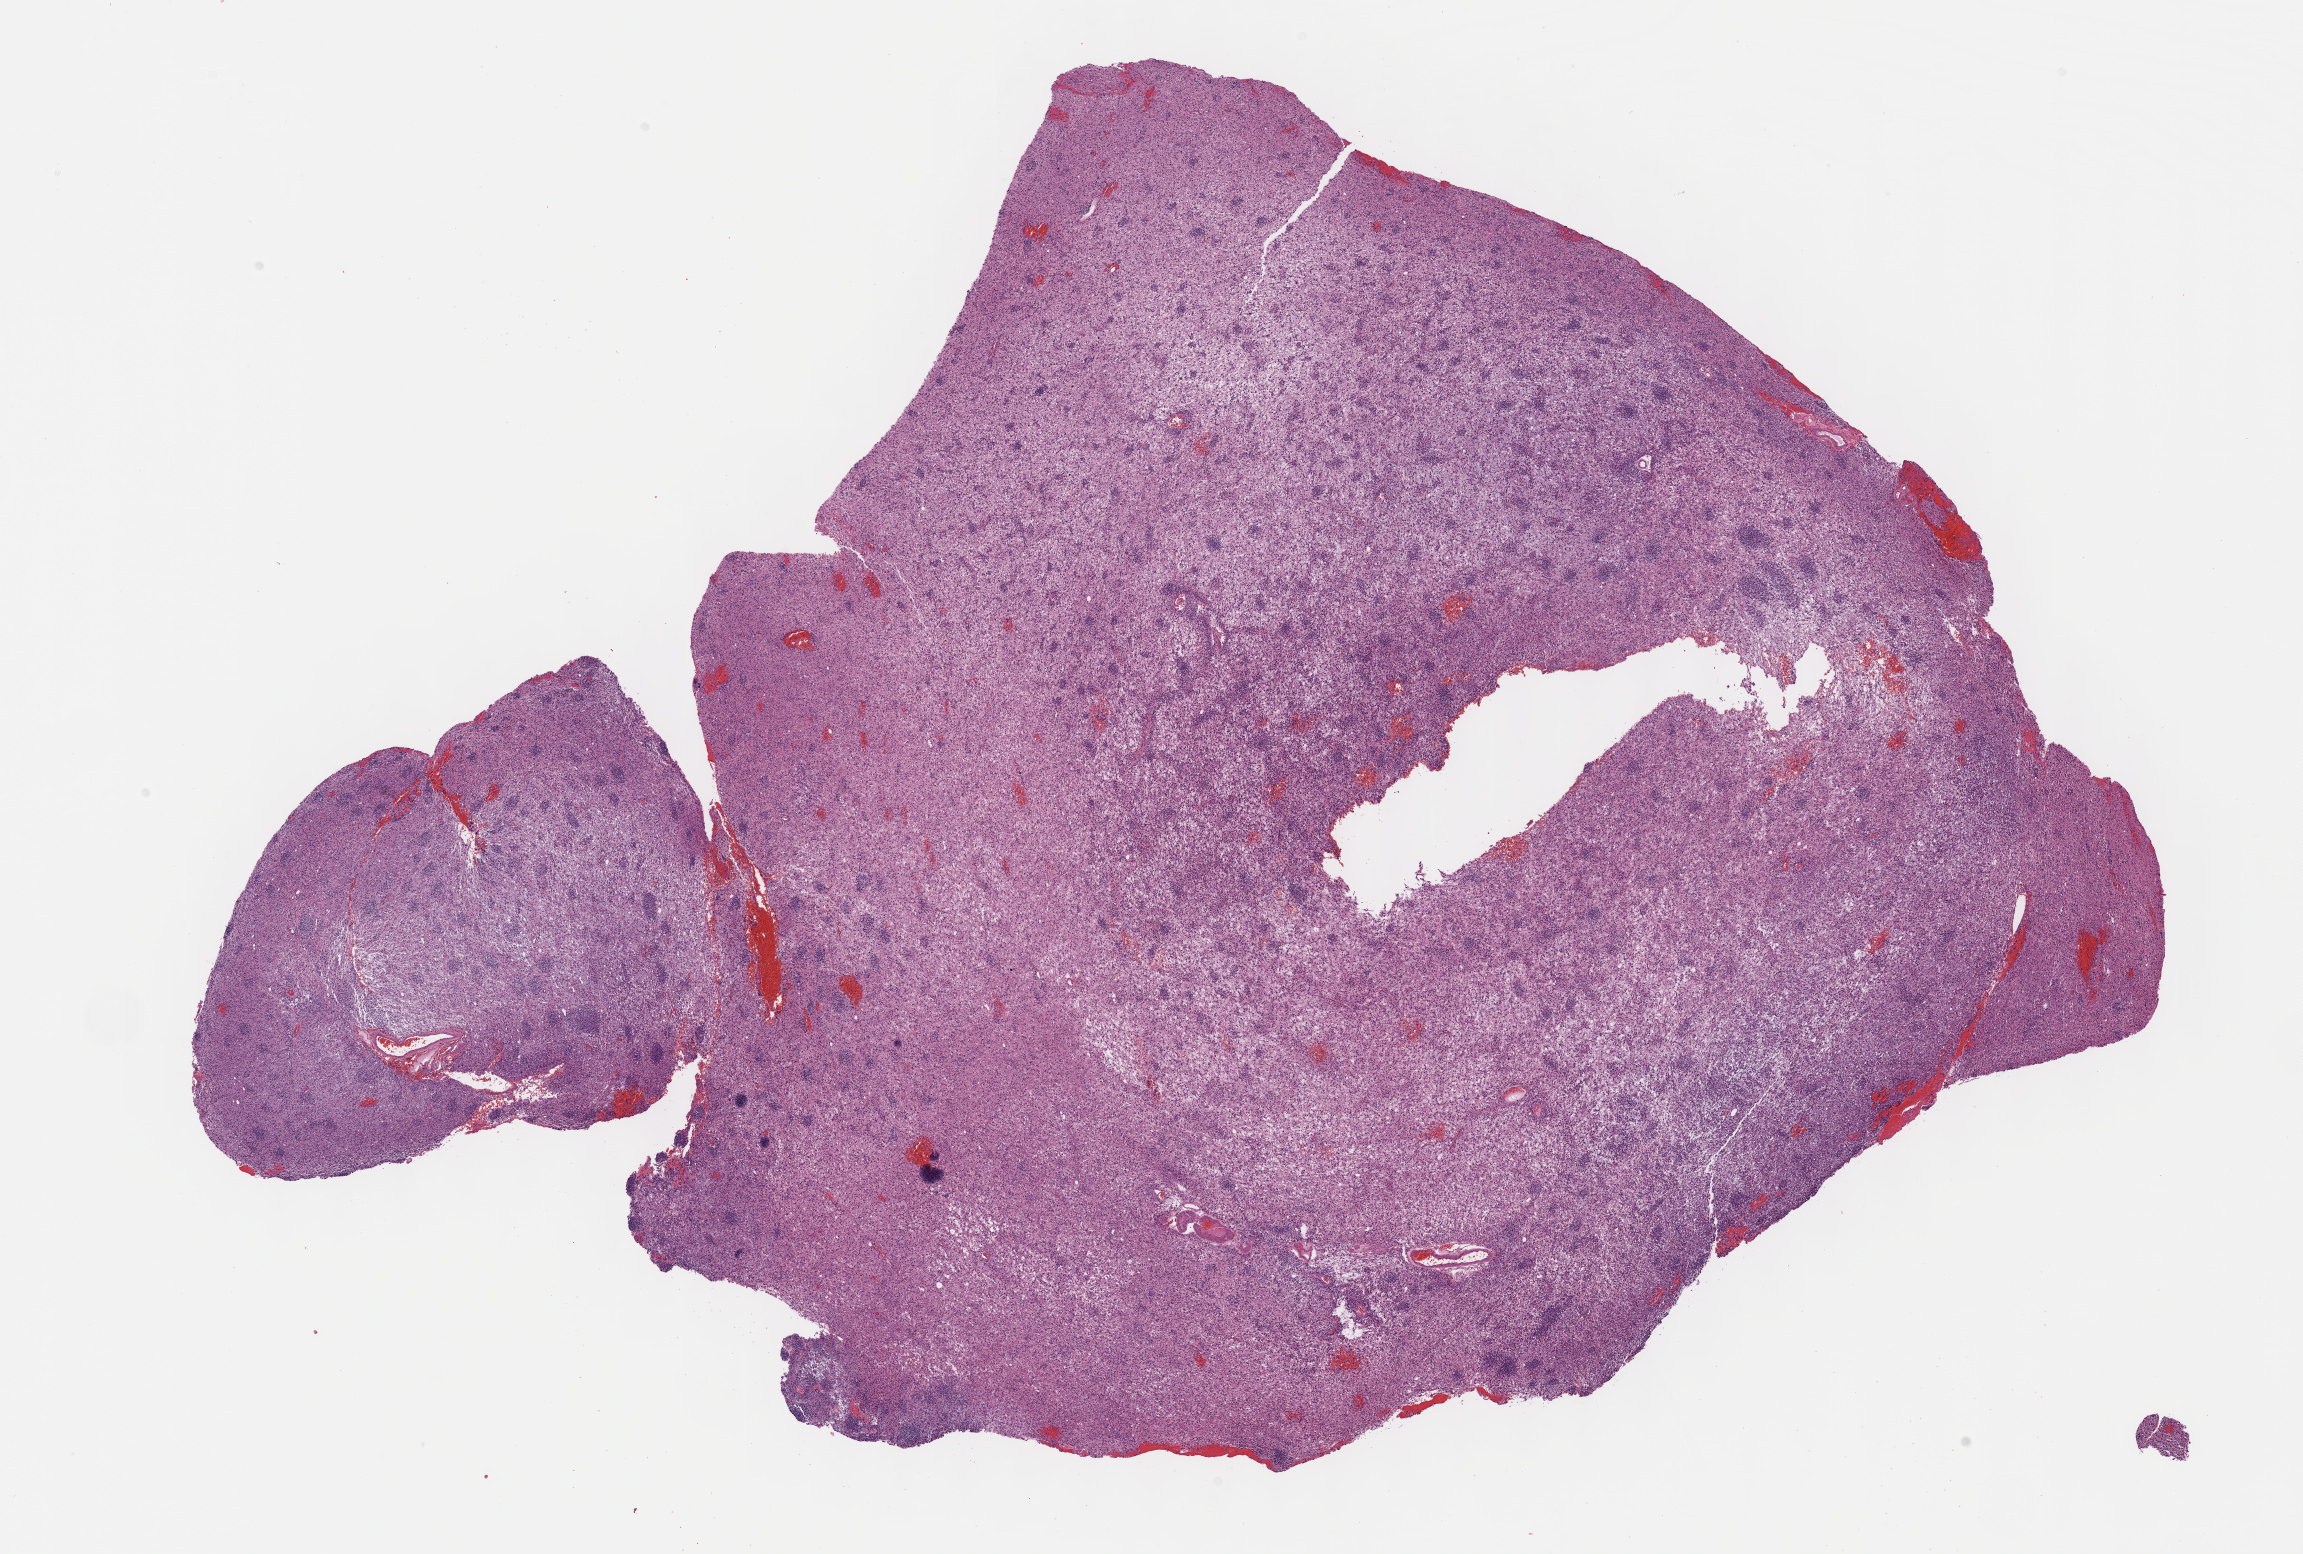
H&E whole-slide image, a low-resolution overview of the entire scanned area, about 18.6 x 12.6 mm, formalin-fixed paraffin-embedded (FFPE) diagnostic section, sample: primary tumour, brain. Patient: male, age at initial diagnosis 67 years. Histologic grade: G3 (poorly differentiated).
Pathologic diagnosis: Mixed glioma.